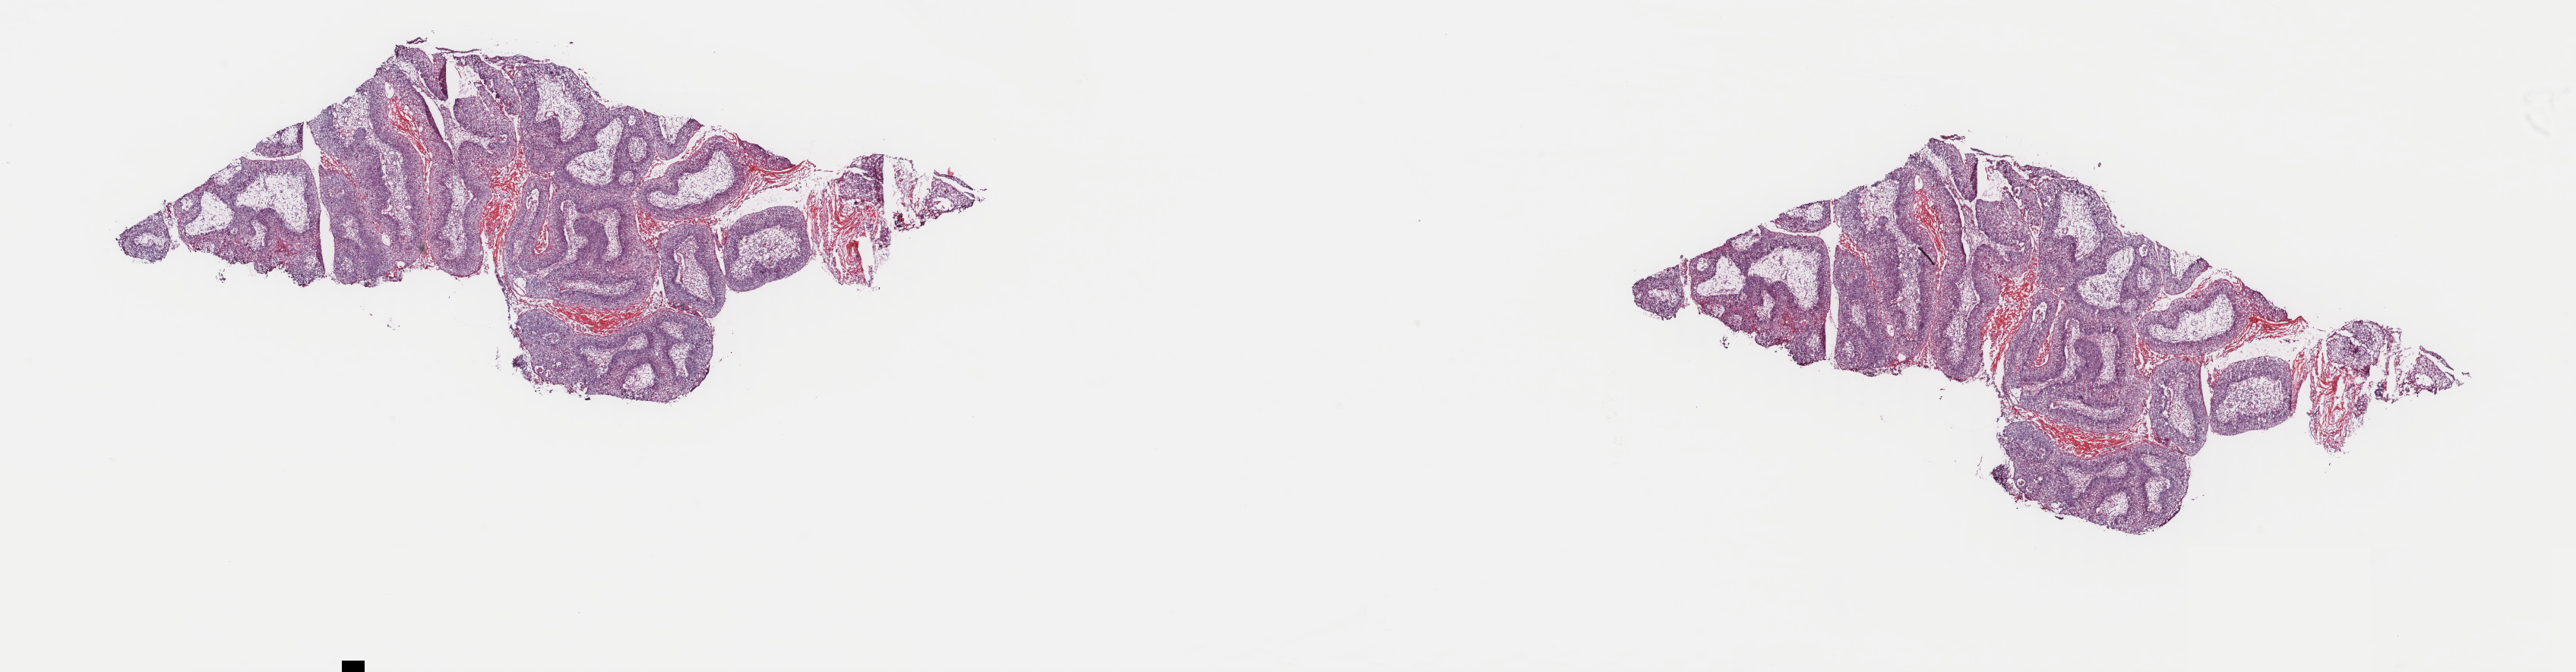
H&E whole-slide image, low-resolution overview of the scanned area, about 26.9 x 7.0 mm (acquisition: 40x scan); frozen section; primary tumour sample from the head and neck. Male patient; age at initial diagnosis 70 years. Pathologist review of this section (percent, as recorded): tumour cells 100%, tumour nuclei 75%.
Histologic diagnosis: Squamous cell carcinoma, NOS (larynx, NOS).